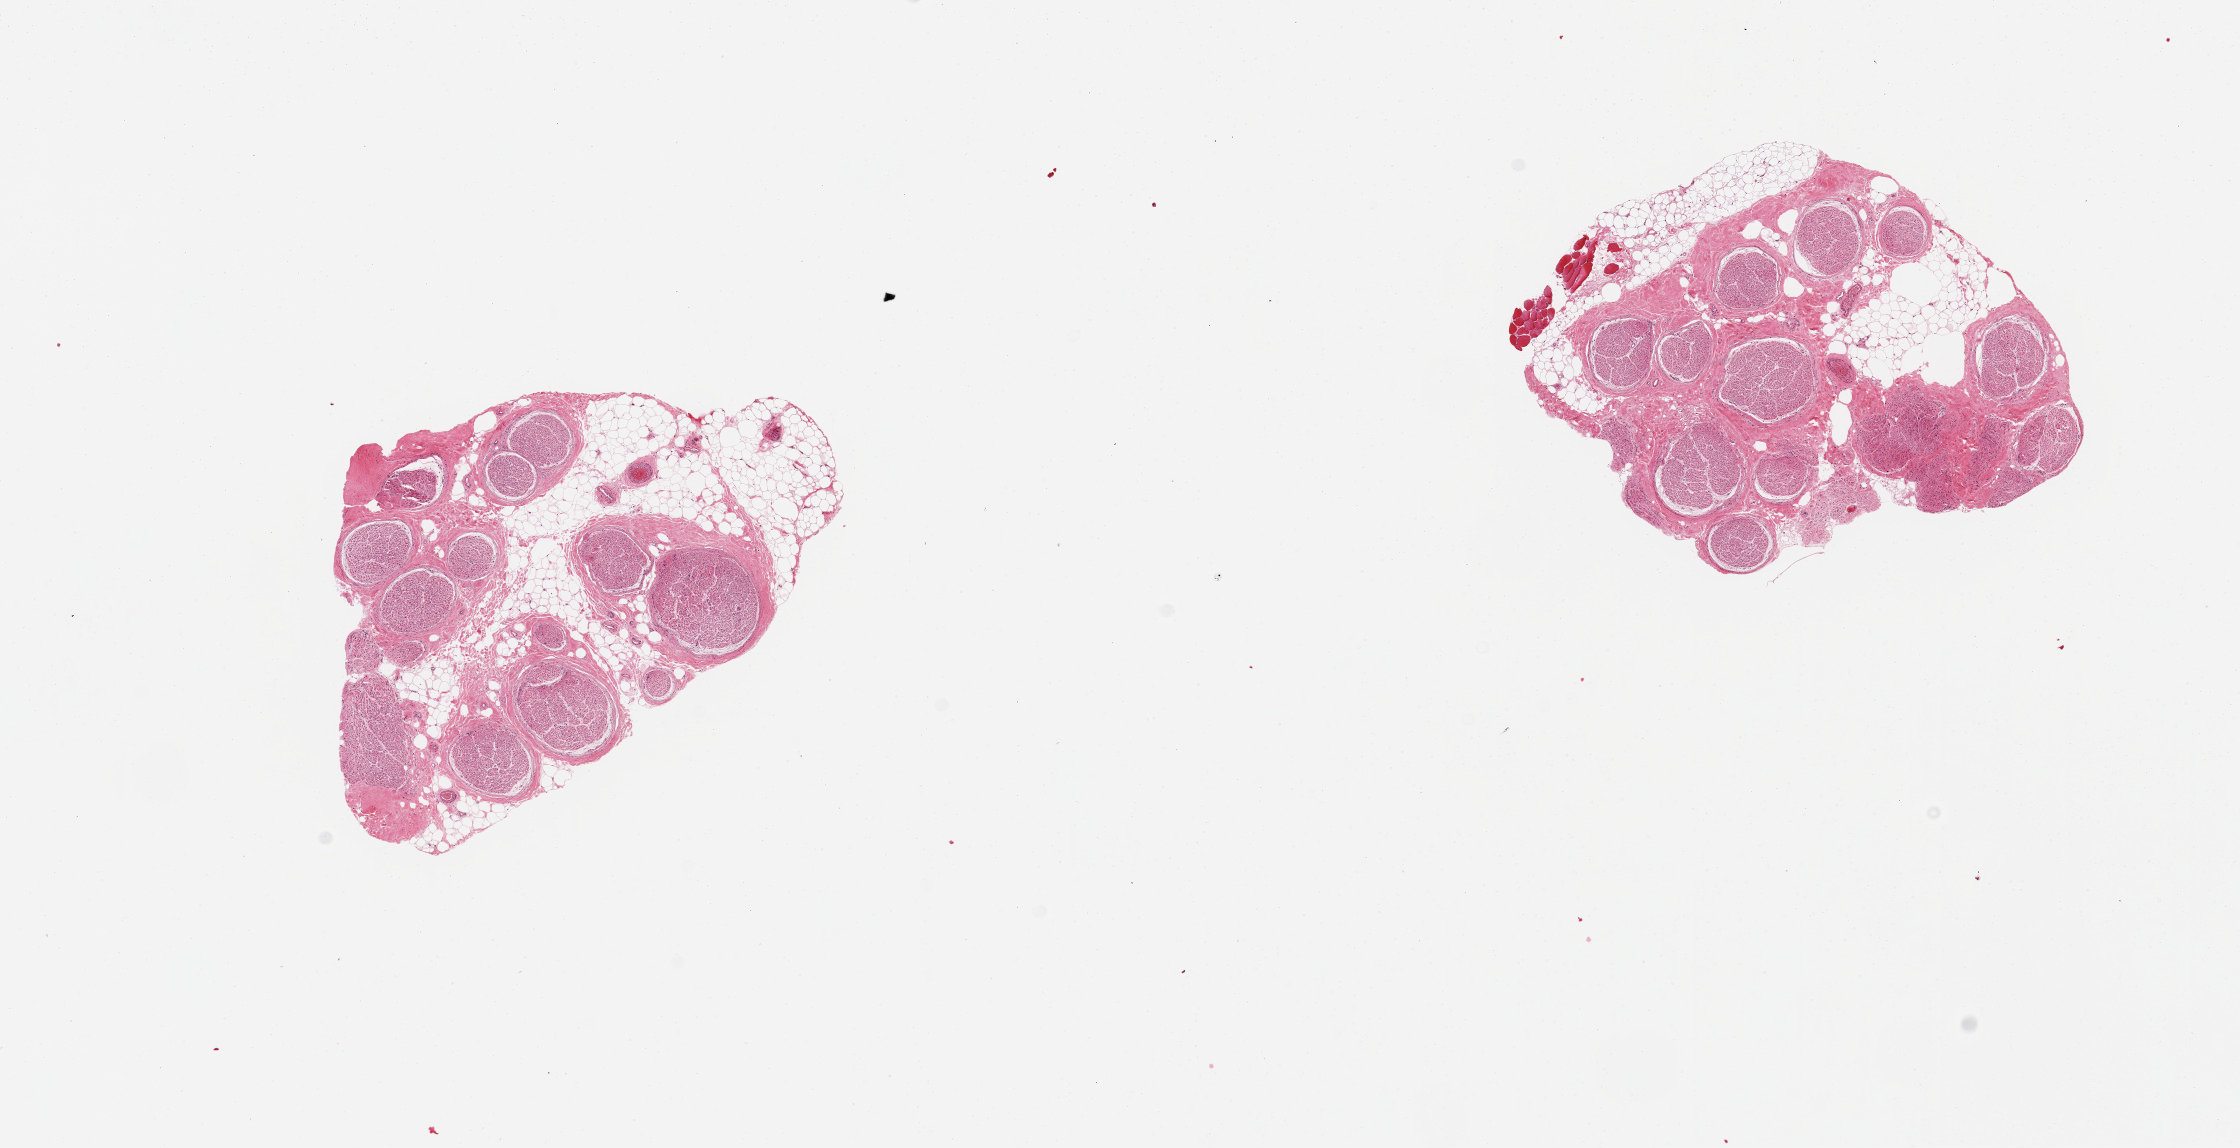
Hematoxylin and eosin (H&E) whole-slide image — a low-resolution overview of the entire scanned area, about 17.7 x 9.1 mm (slide scanned at 20x); PAXgene-fixed paraffin-embedded (PFPE) section; section of tibial nerve (target tissue); donor tissue sample. Male donor.
• pathologist's review note for this sample: 2 pieces; 40% internal & external fat